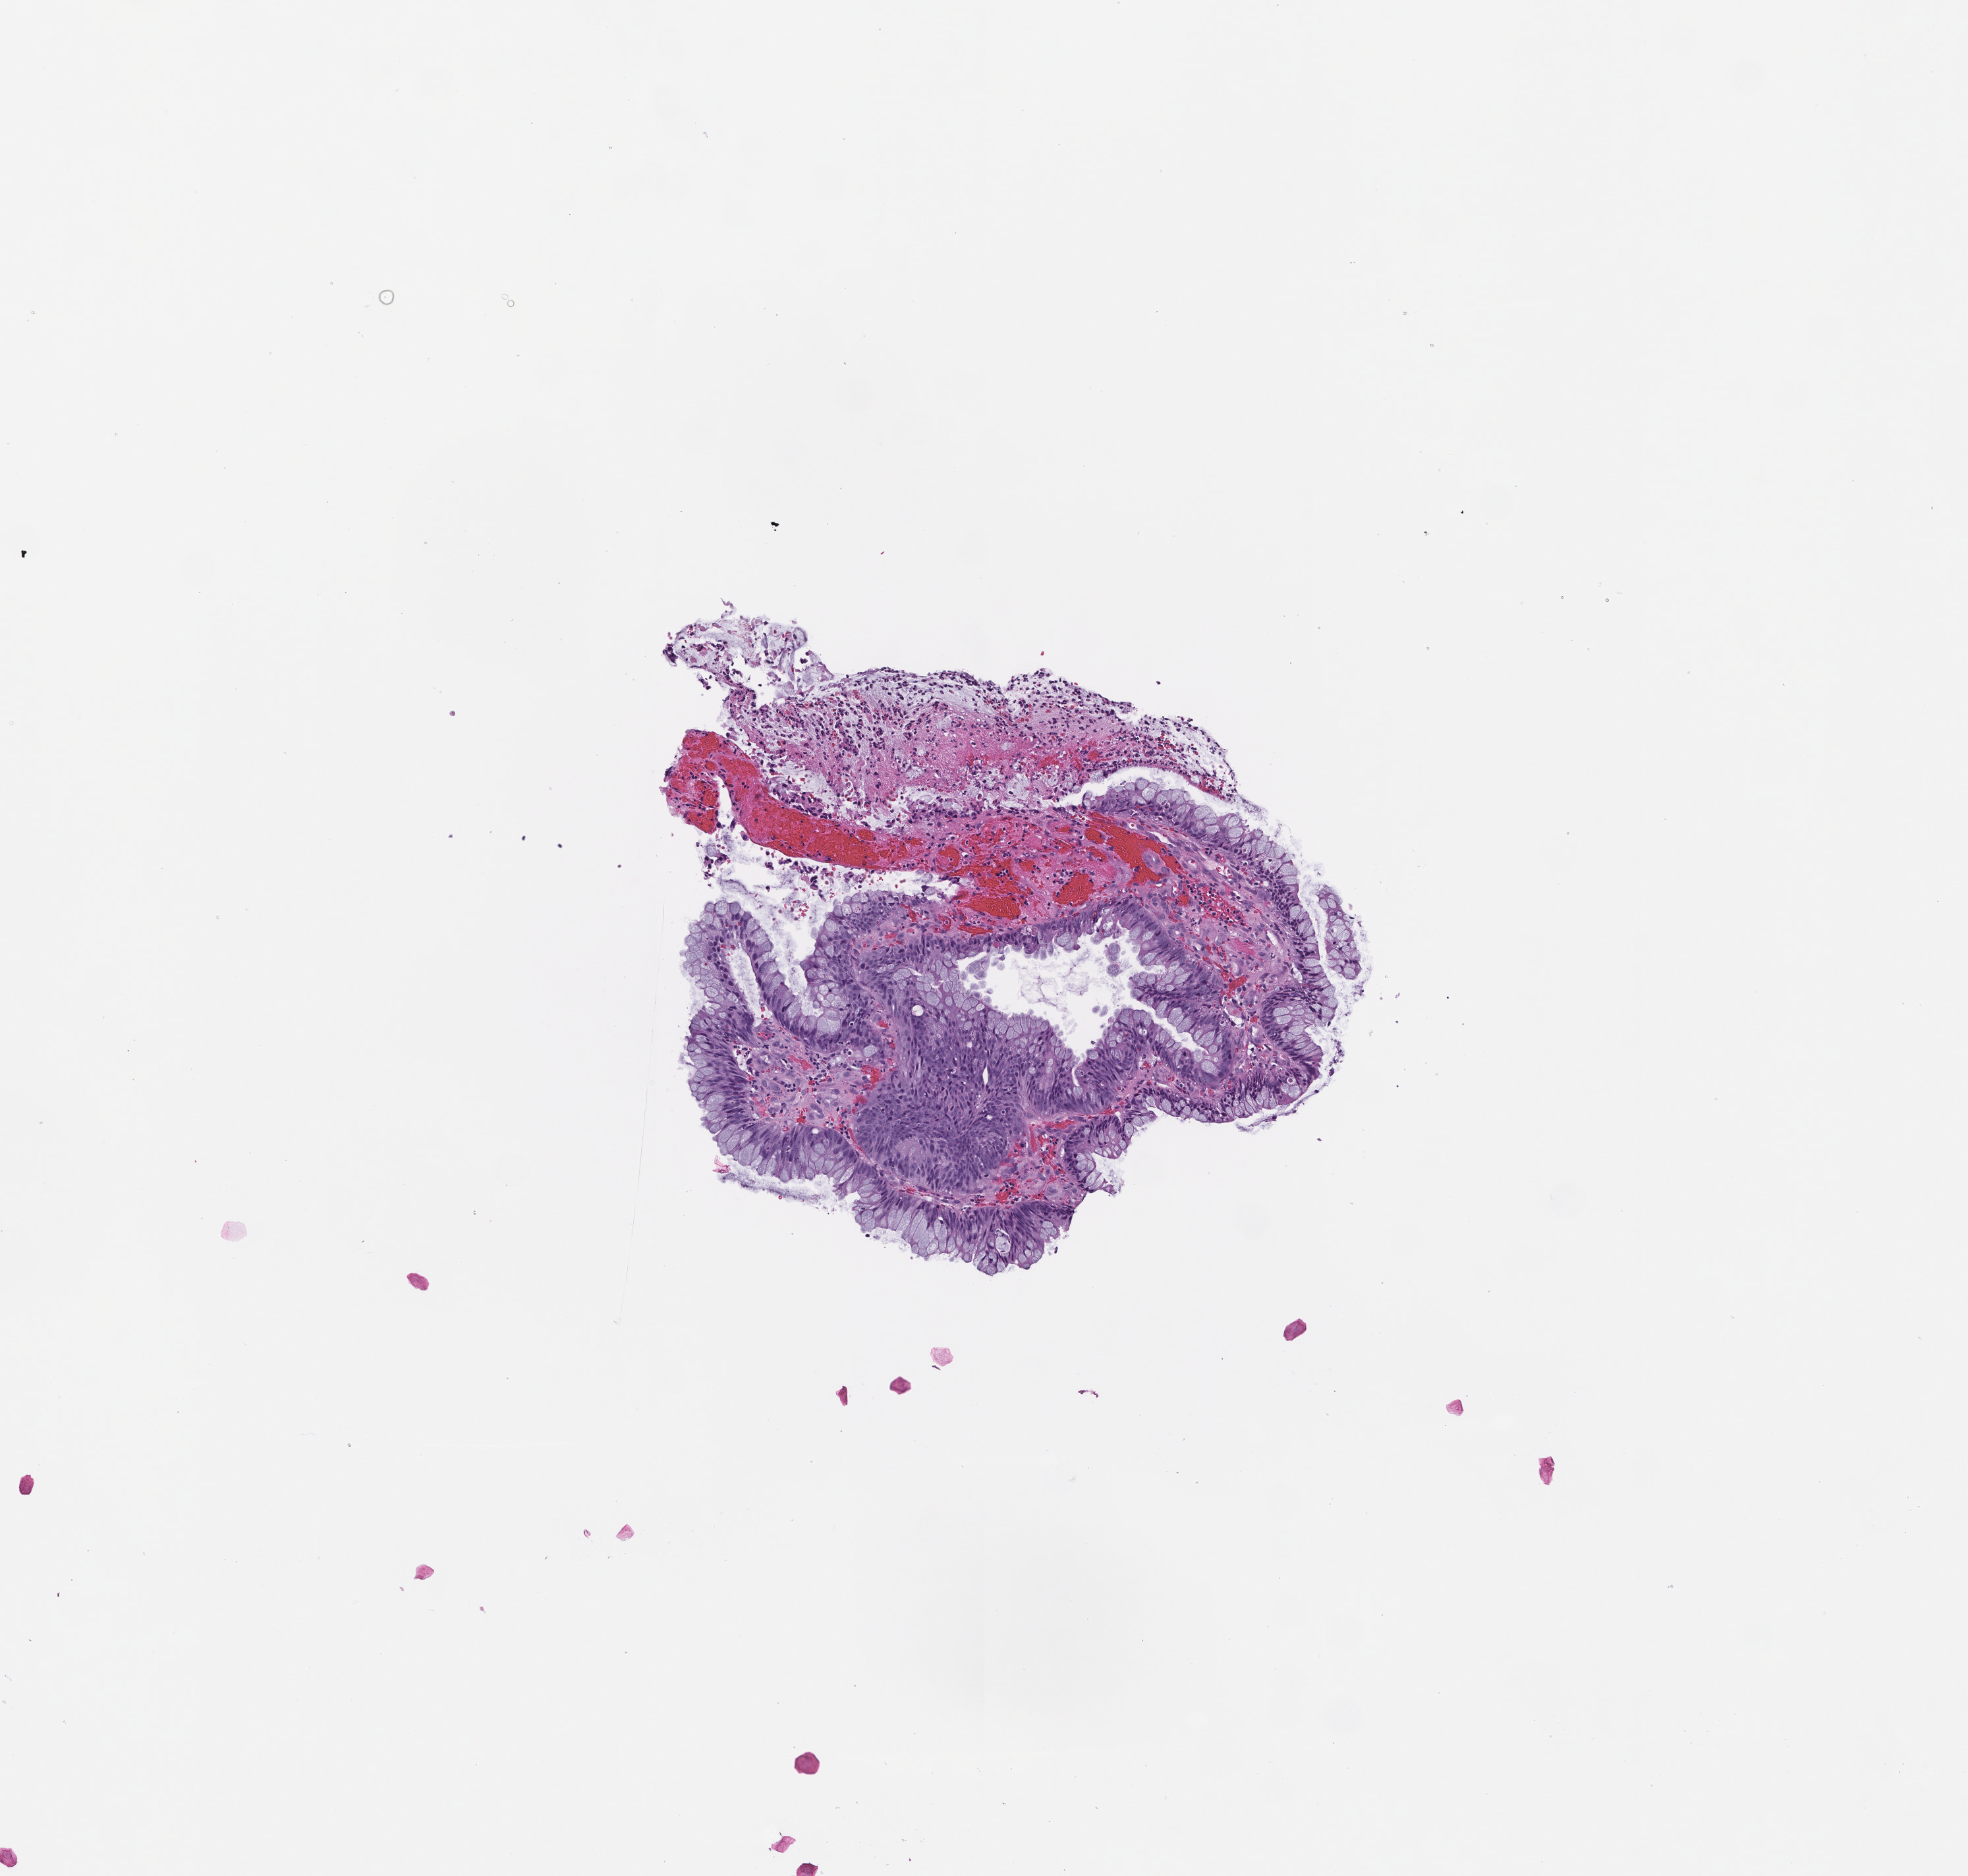
Hematoxylin and eosin (H&E) whole-slide image — low-resolution overview of the scanned area, about 3.0 x 2.9 mm; FFPE section; site: colon; specimen time point: archival tissue. Patient sex: male.
This section: primary tumor. Diagnosis: Colorectal Carcinoma.